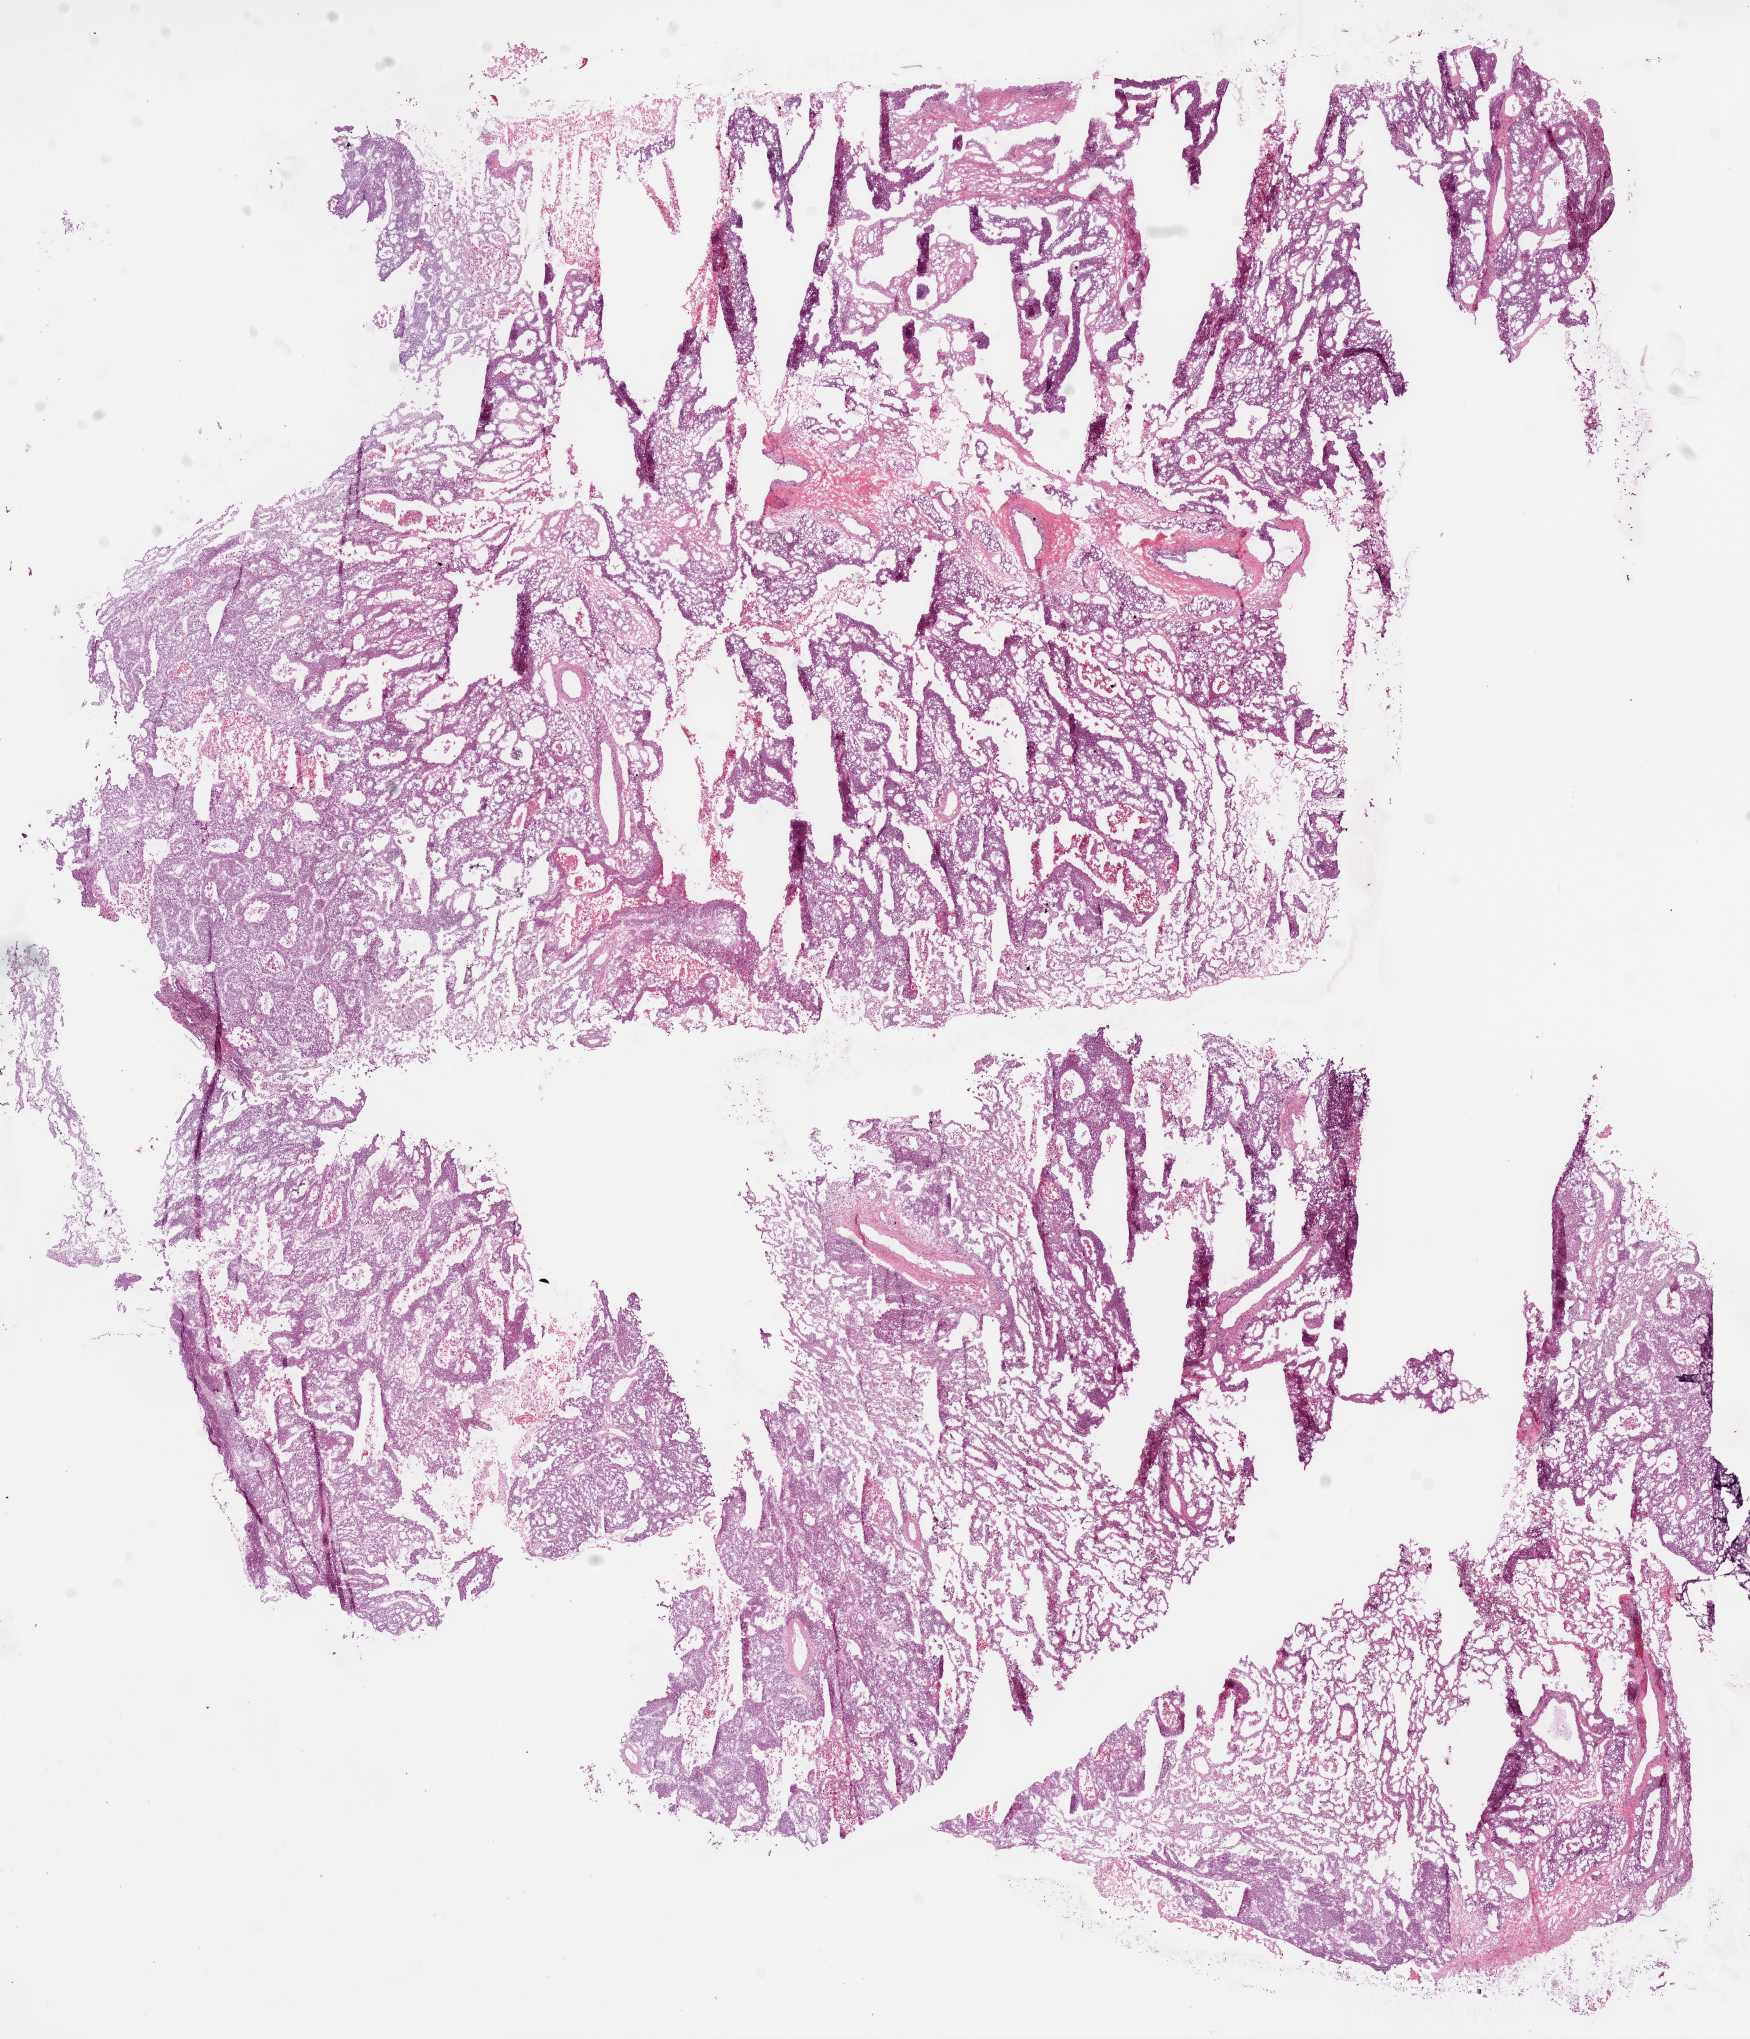
H&E-stained whole-slide image — low-resolution overview of the scanned area, about 14.0 x 16.4 mm, frozen section from the bottom of the tissue portion, primary tumour sample from the lung. Male, age 65 years at initial diagnosis. Slide review estimates, as recorded: tumour cells 77%, tumour nuclei 75%.
Histologic diagnosis: Squamous cell carcinoma, NOS.